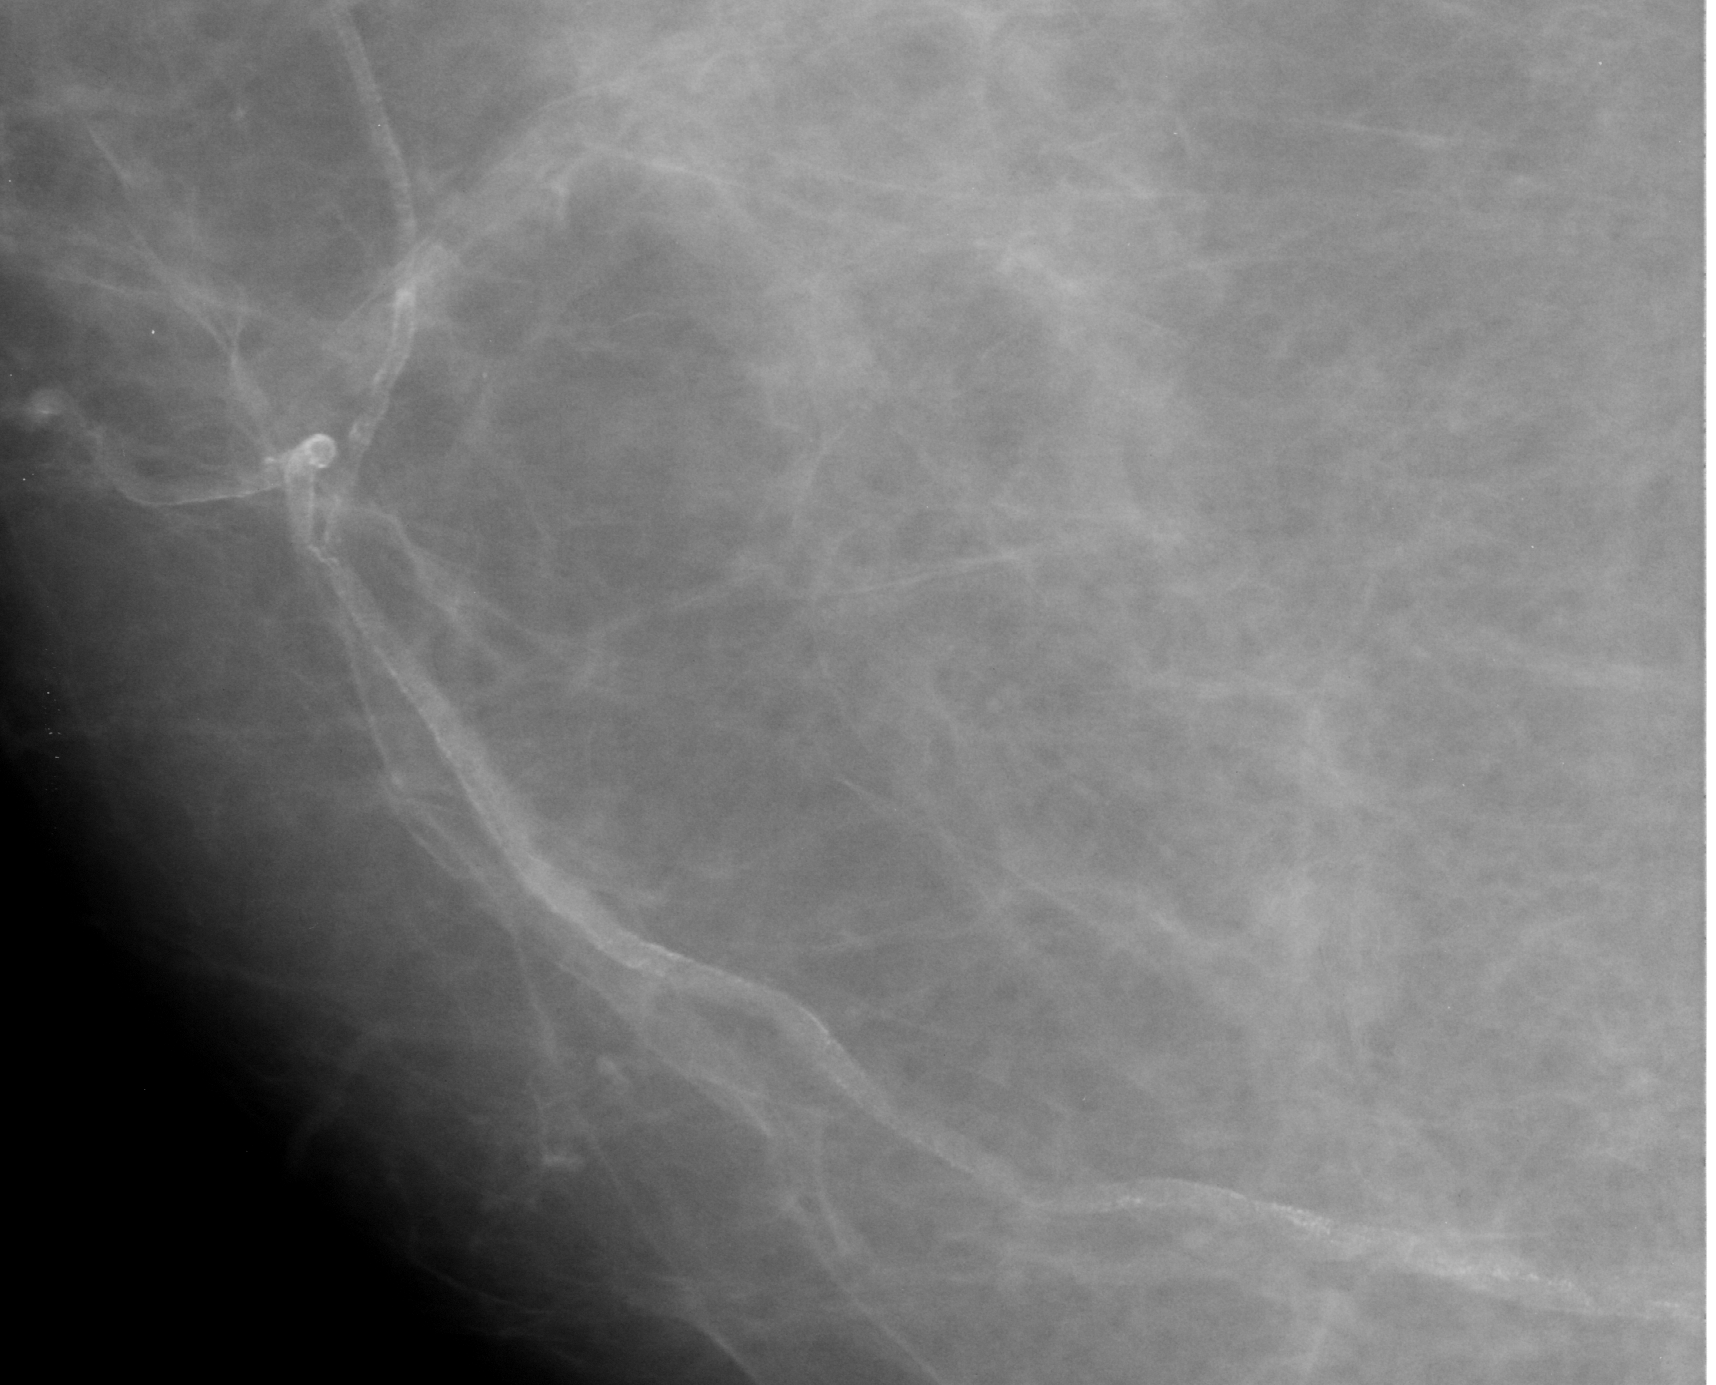
Region of interest cut from a scanned film mammogram (one marked finding), right breast, CC view.
Finding: calcifications, morphology vascular; BI-RADS assessment category 2; subtlety rating 3 on a 1 (subtle) to 5 (obvious) scale; benign; no additional work-up was recommended (benign without callback).